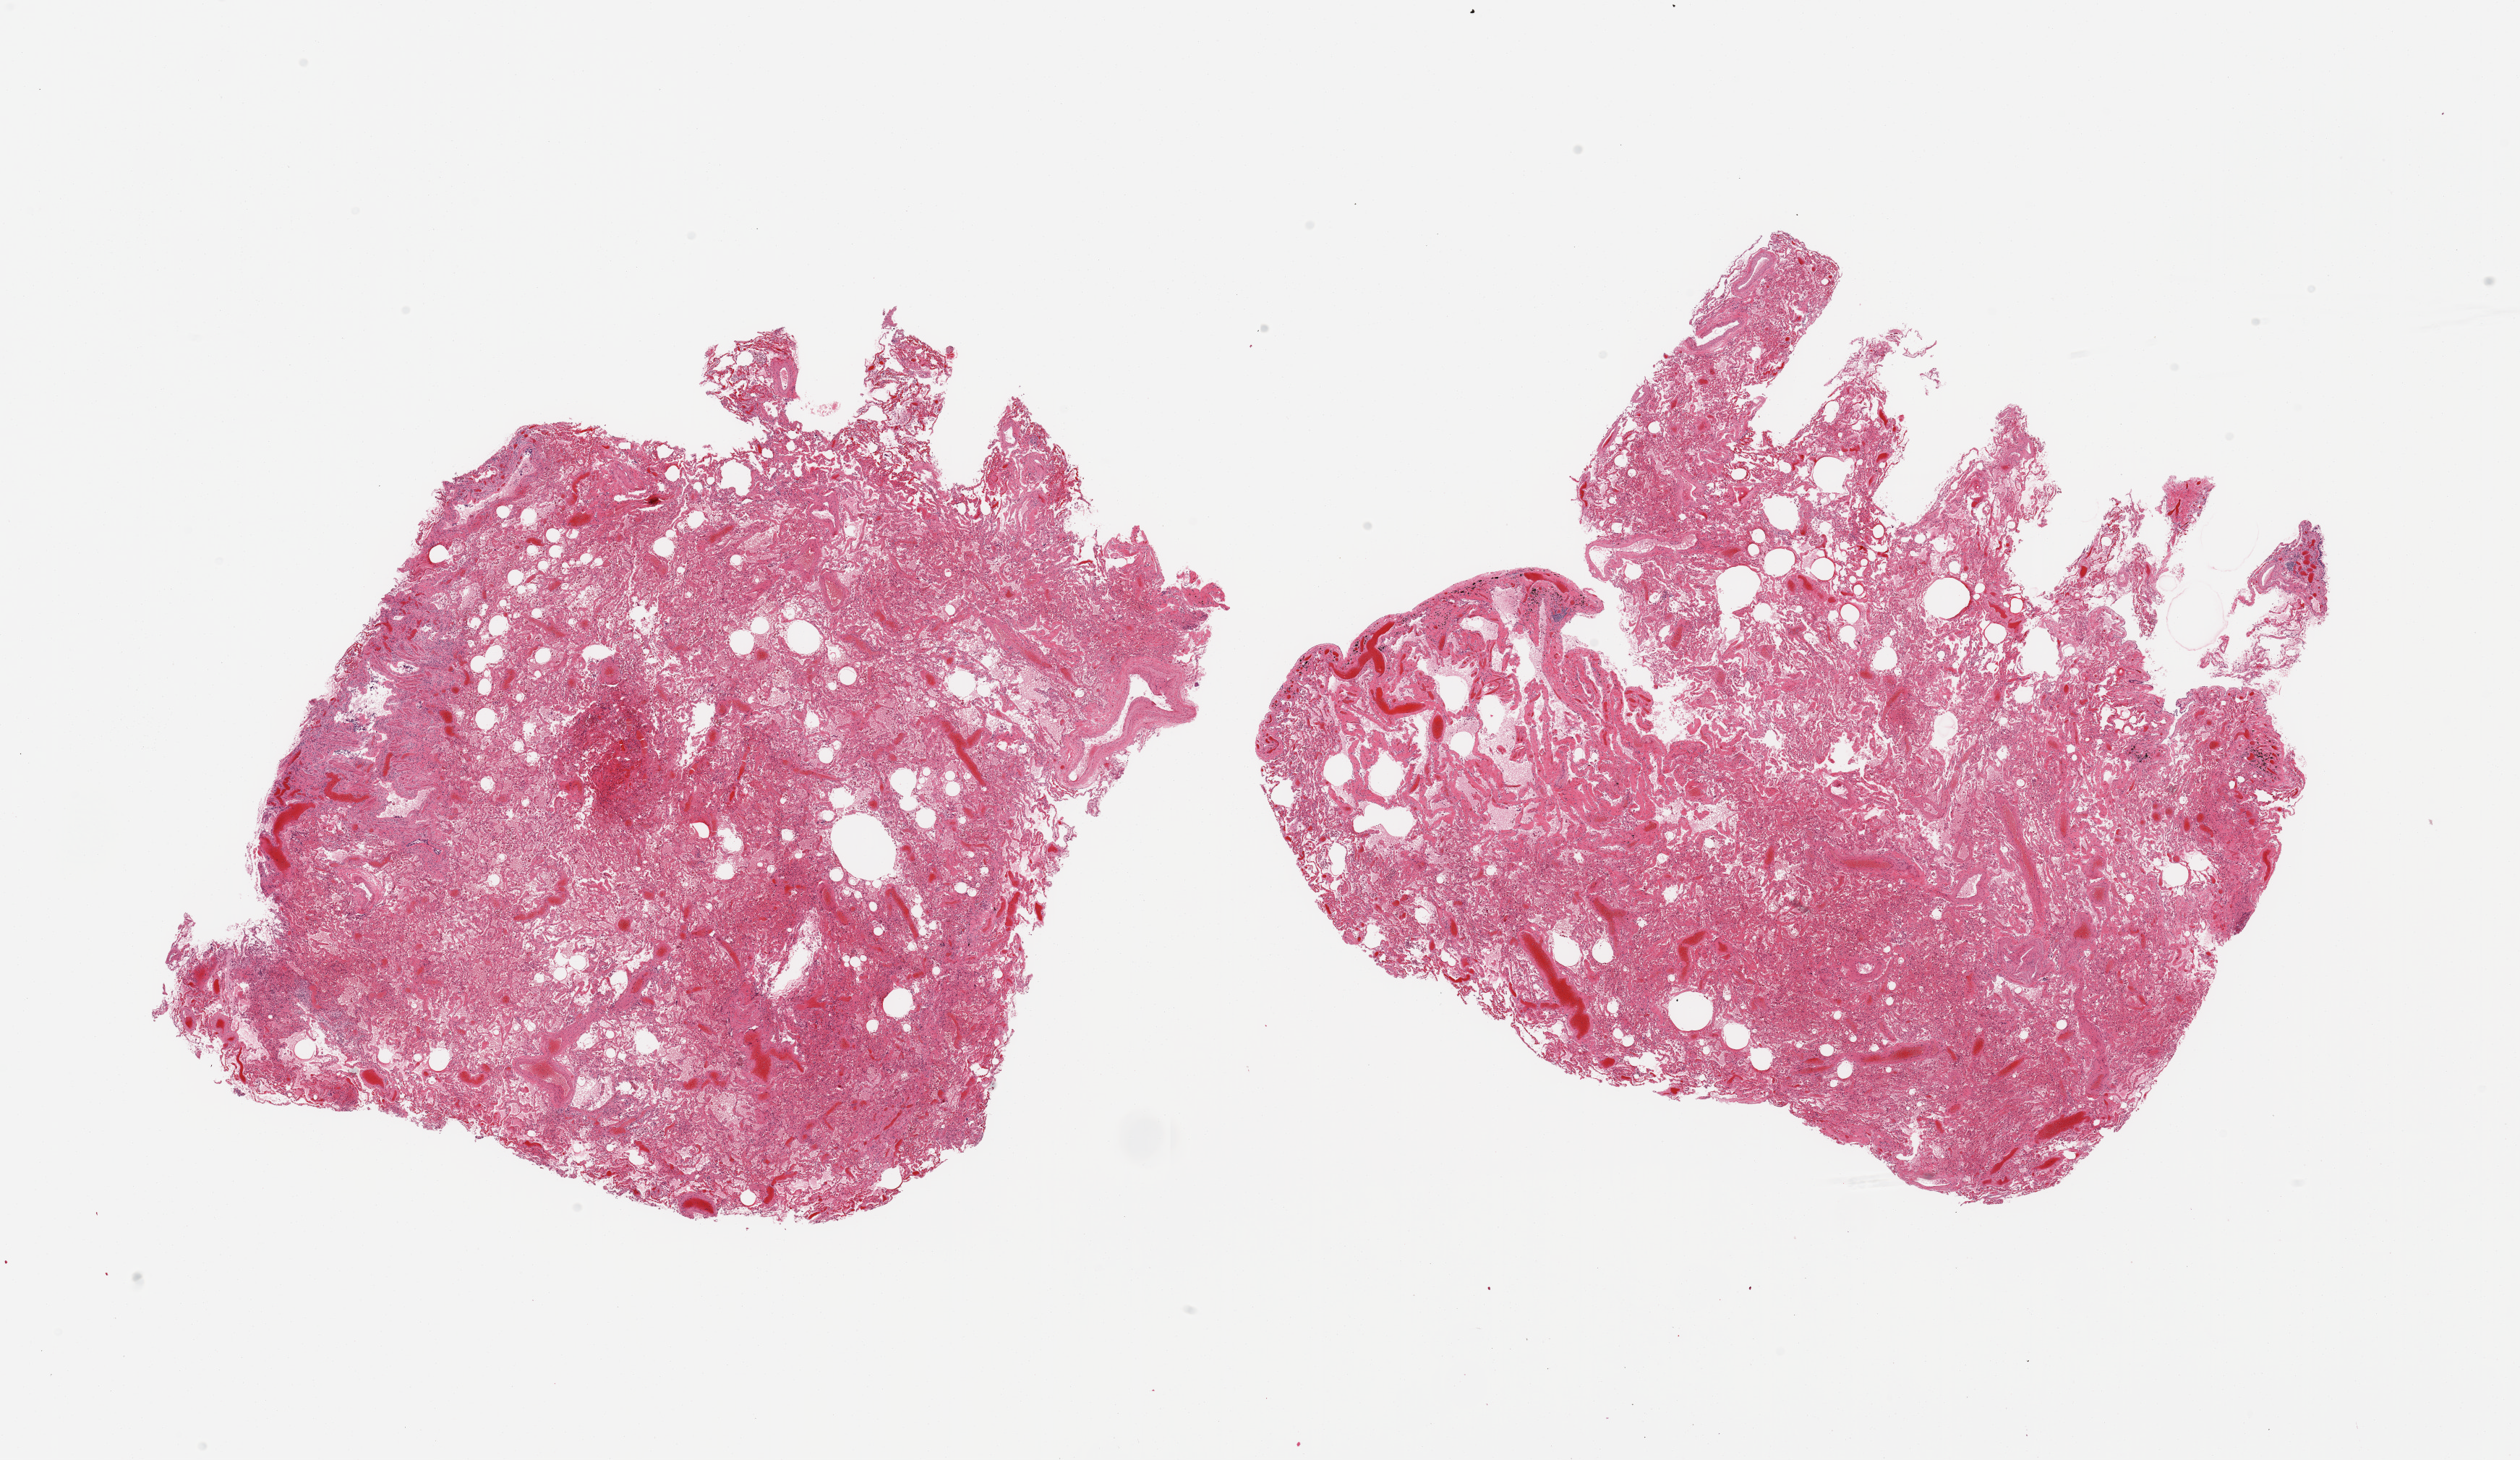
Whole-slide image, hematoxylin and eosin (H&E) stain, shown as a low-resolution overview of the whole scanned area (about 27.6 x 16.0 mm, slide scanned at 20x). PAXgene-fixed paraffin-embedded (PFPE) section. Target tissue: lung. Donor tissue sample. Donor: male.
Reviewer comment on this tissue sample: 2 pieces; congestion, edema, 1 piece includes portion of pleura (not target), some fibrosis.